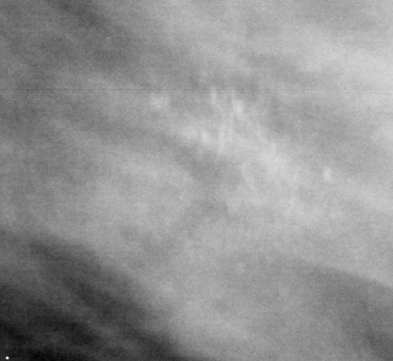
Cropped region of a digitized screen-film mammogram centred on a radiologist-marked abnormality, left breast, MLO view.
Calcifications, morphology pleomorphic, distribution clustered; BI-RADS assessment category 3; pathology (as recorded): malignant.